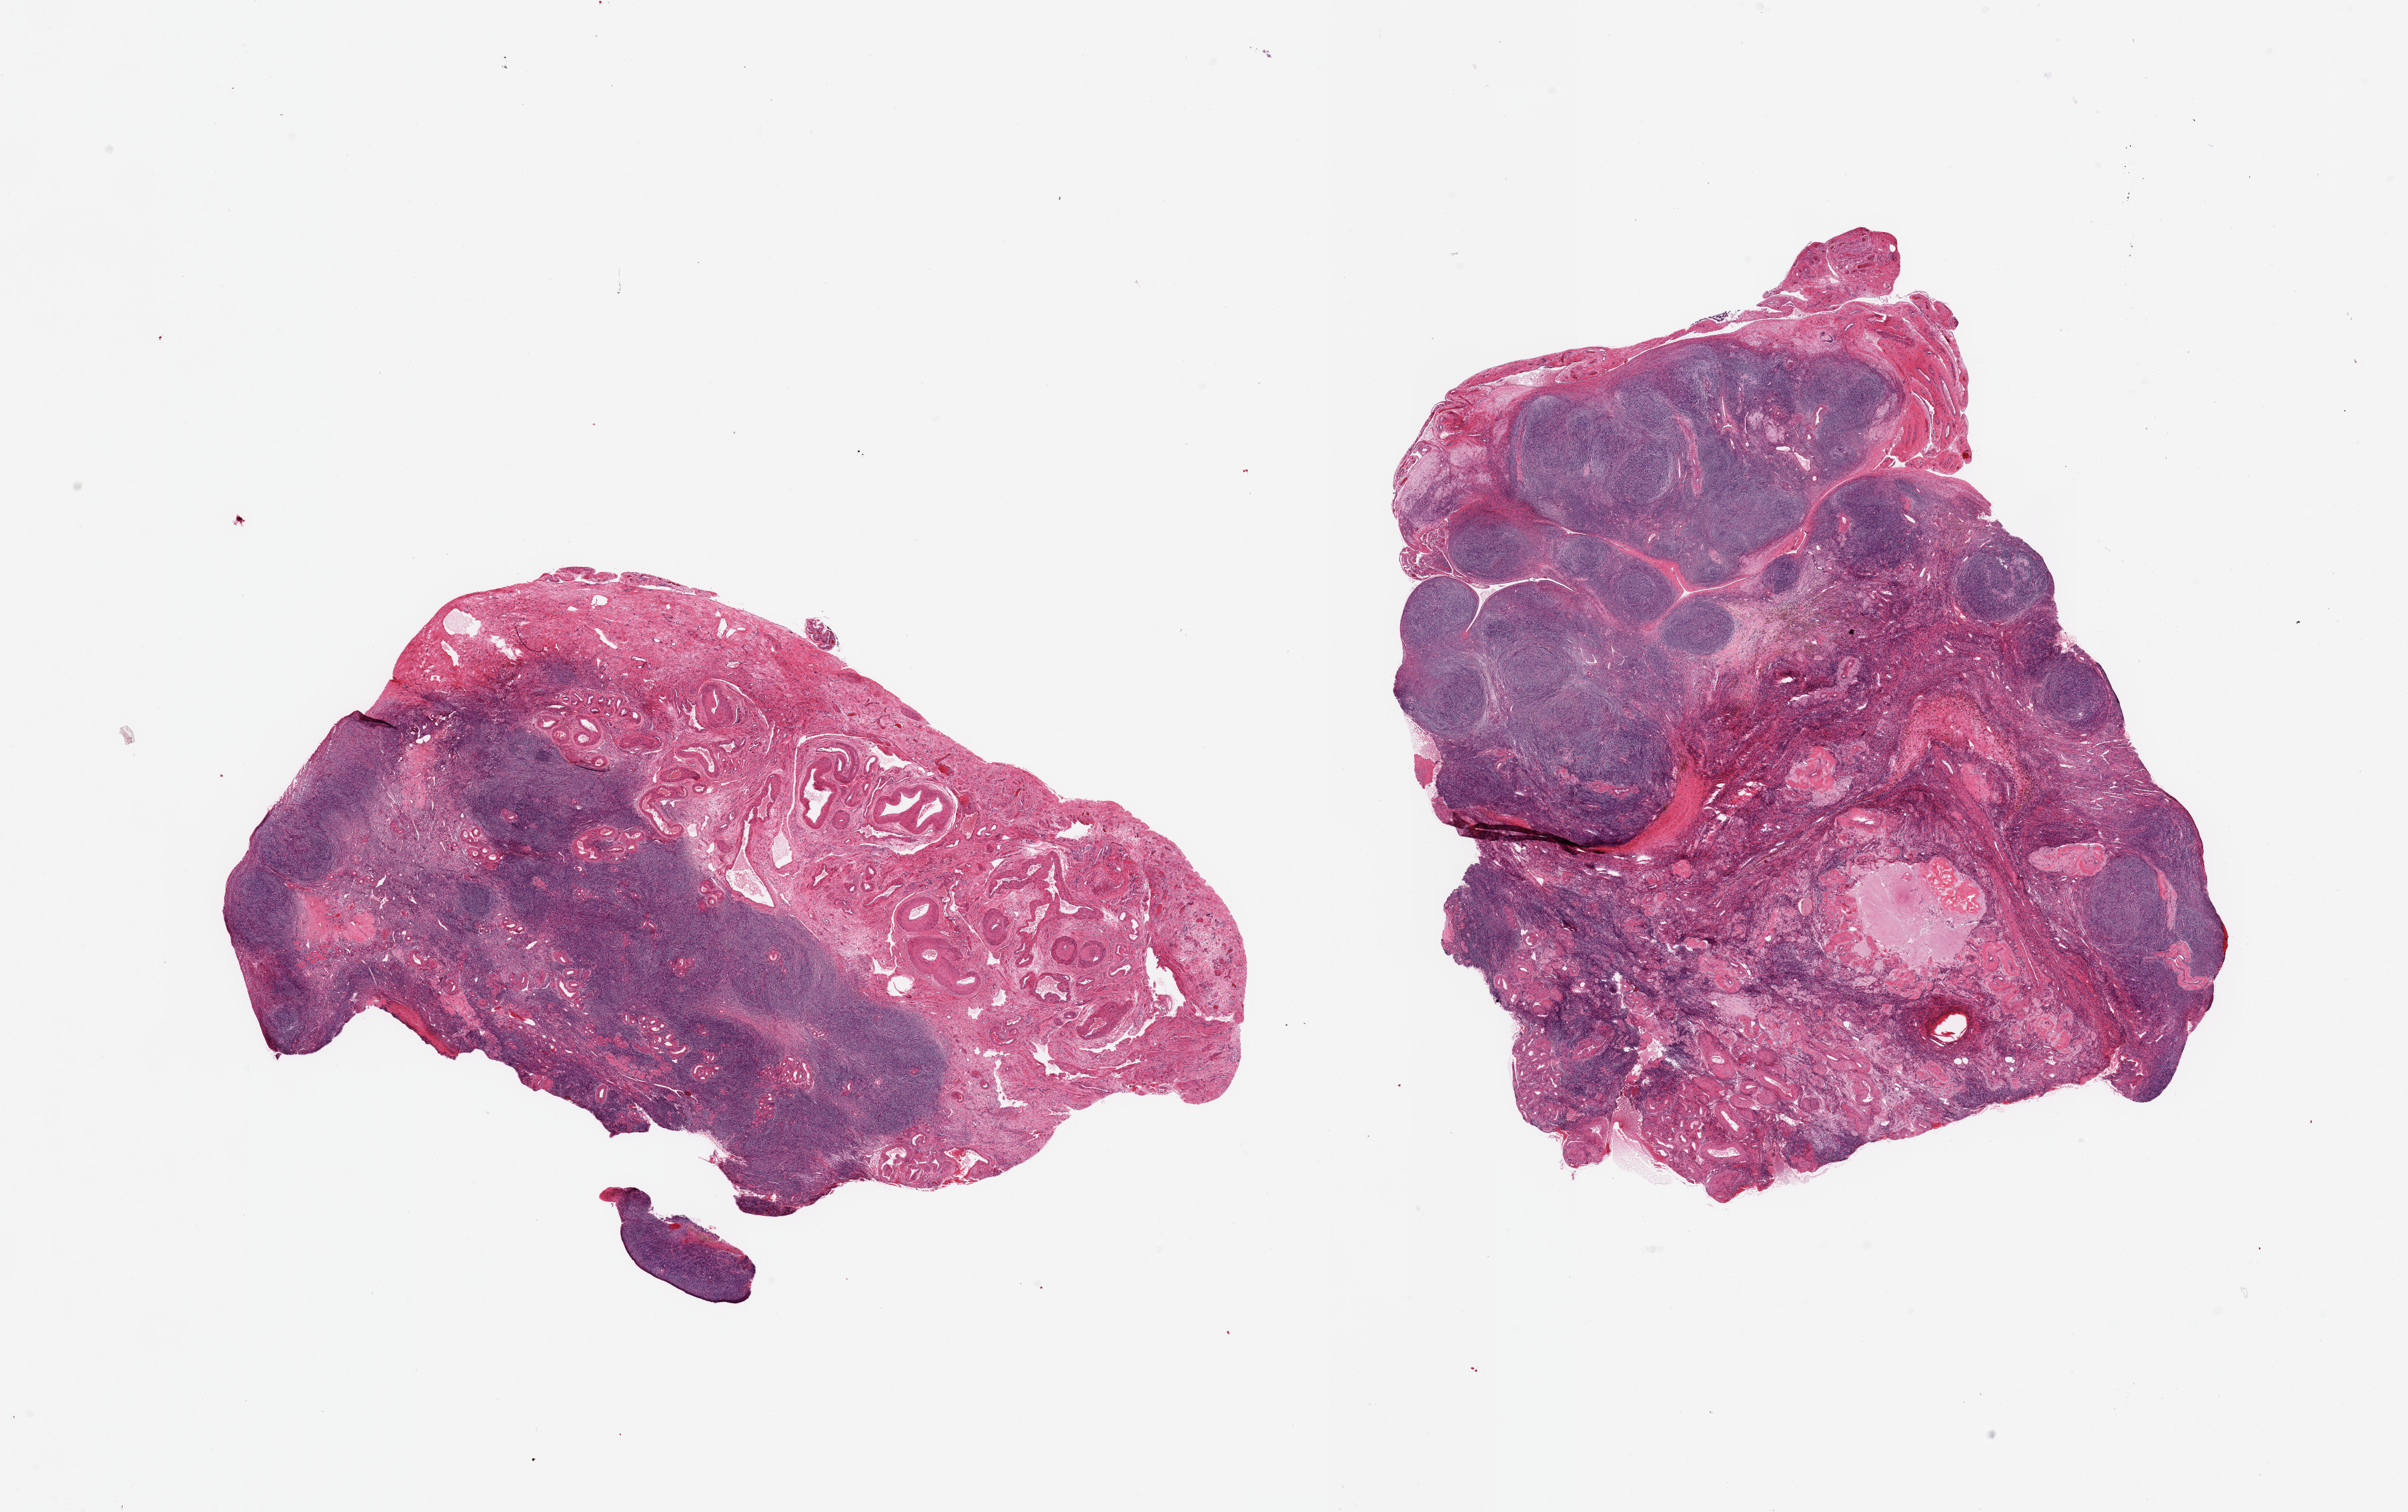
Whole-slide image, haematoxylin and eosin stain, whole scanned area (about 28.5 x 17.9 mm) shown as a low-resolution overview. PAXgene-fixed paraffin-embedded (PFPE) section. Section of ovary (target tissue). Donor tissue sample. Female donor.
* pathologist's review note for this sample: 2 pieces, ~50% target ovarian stroma, post menopausal atrophic changes; rest is hilar vessel/connective tissues